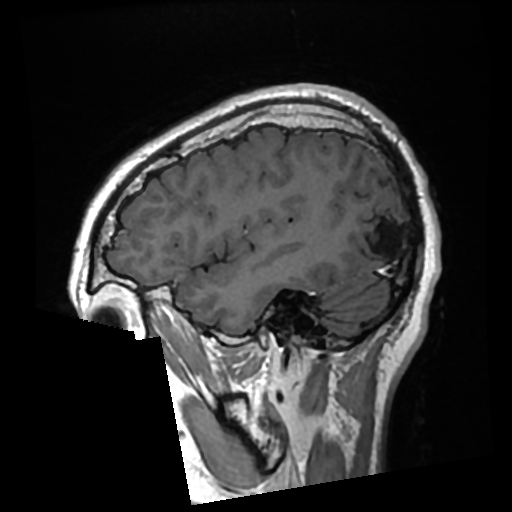
Brain MRI from a brain-tumour surgery series, one sagittal slice; position 78 of 276 along the scan axis; T1-weighted post-contrast; 0.7 mm slice thickness; 512 × 512 image matrix, field of view 250 × 250 mm. Case-level facts recorded for this patient, not image findings: histopathology: Glioma with ependymal features; WHO grade: 2; tumour location: Left Parietal.
Outlined on this slice (manually delineated by an expert):
- previous resection cavity: bounding box (x1, y1, x2, y2) in pixels: (357, 220, 397, 257)